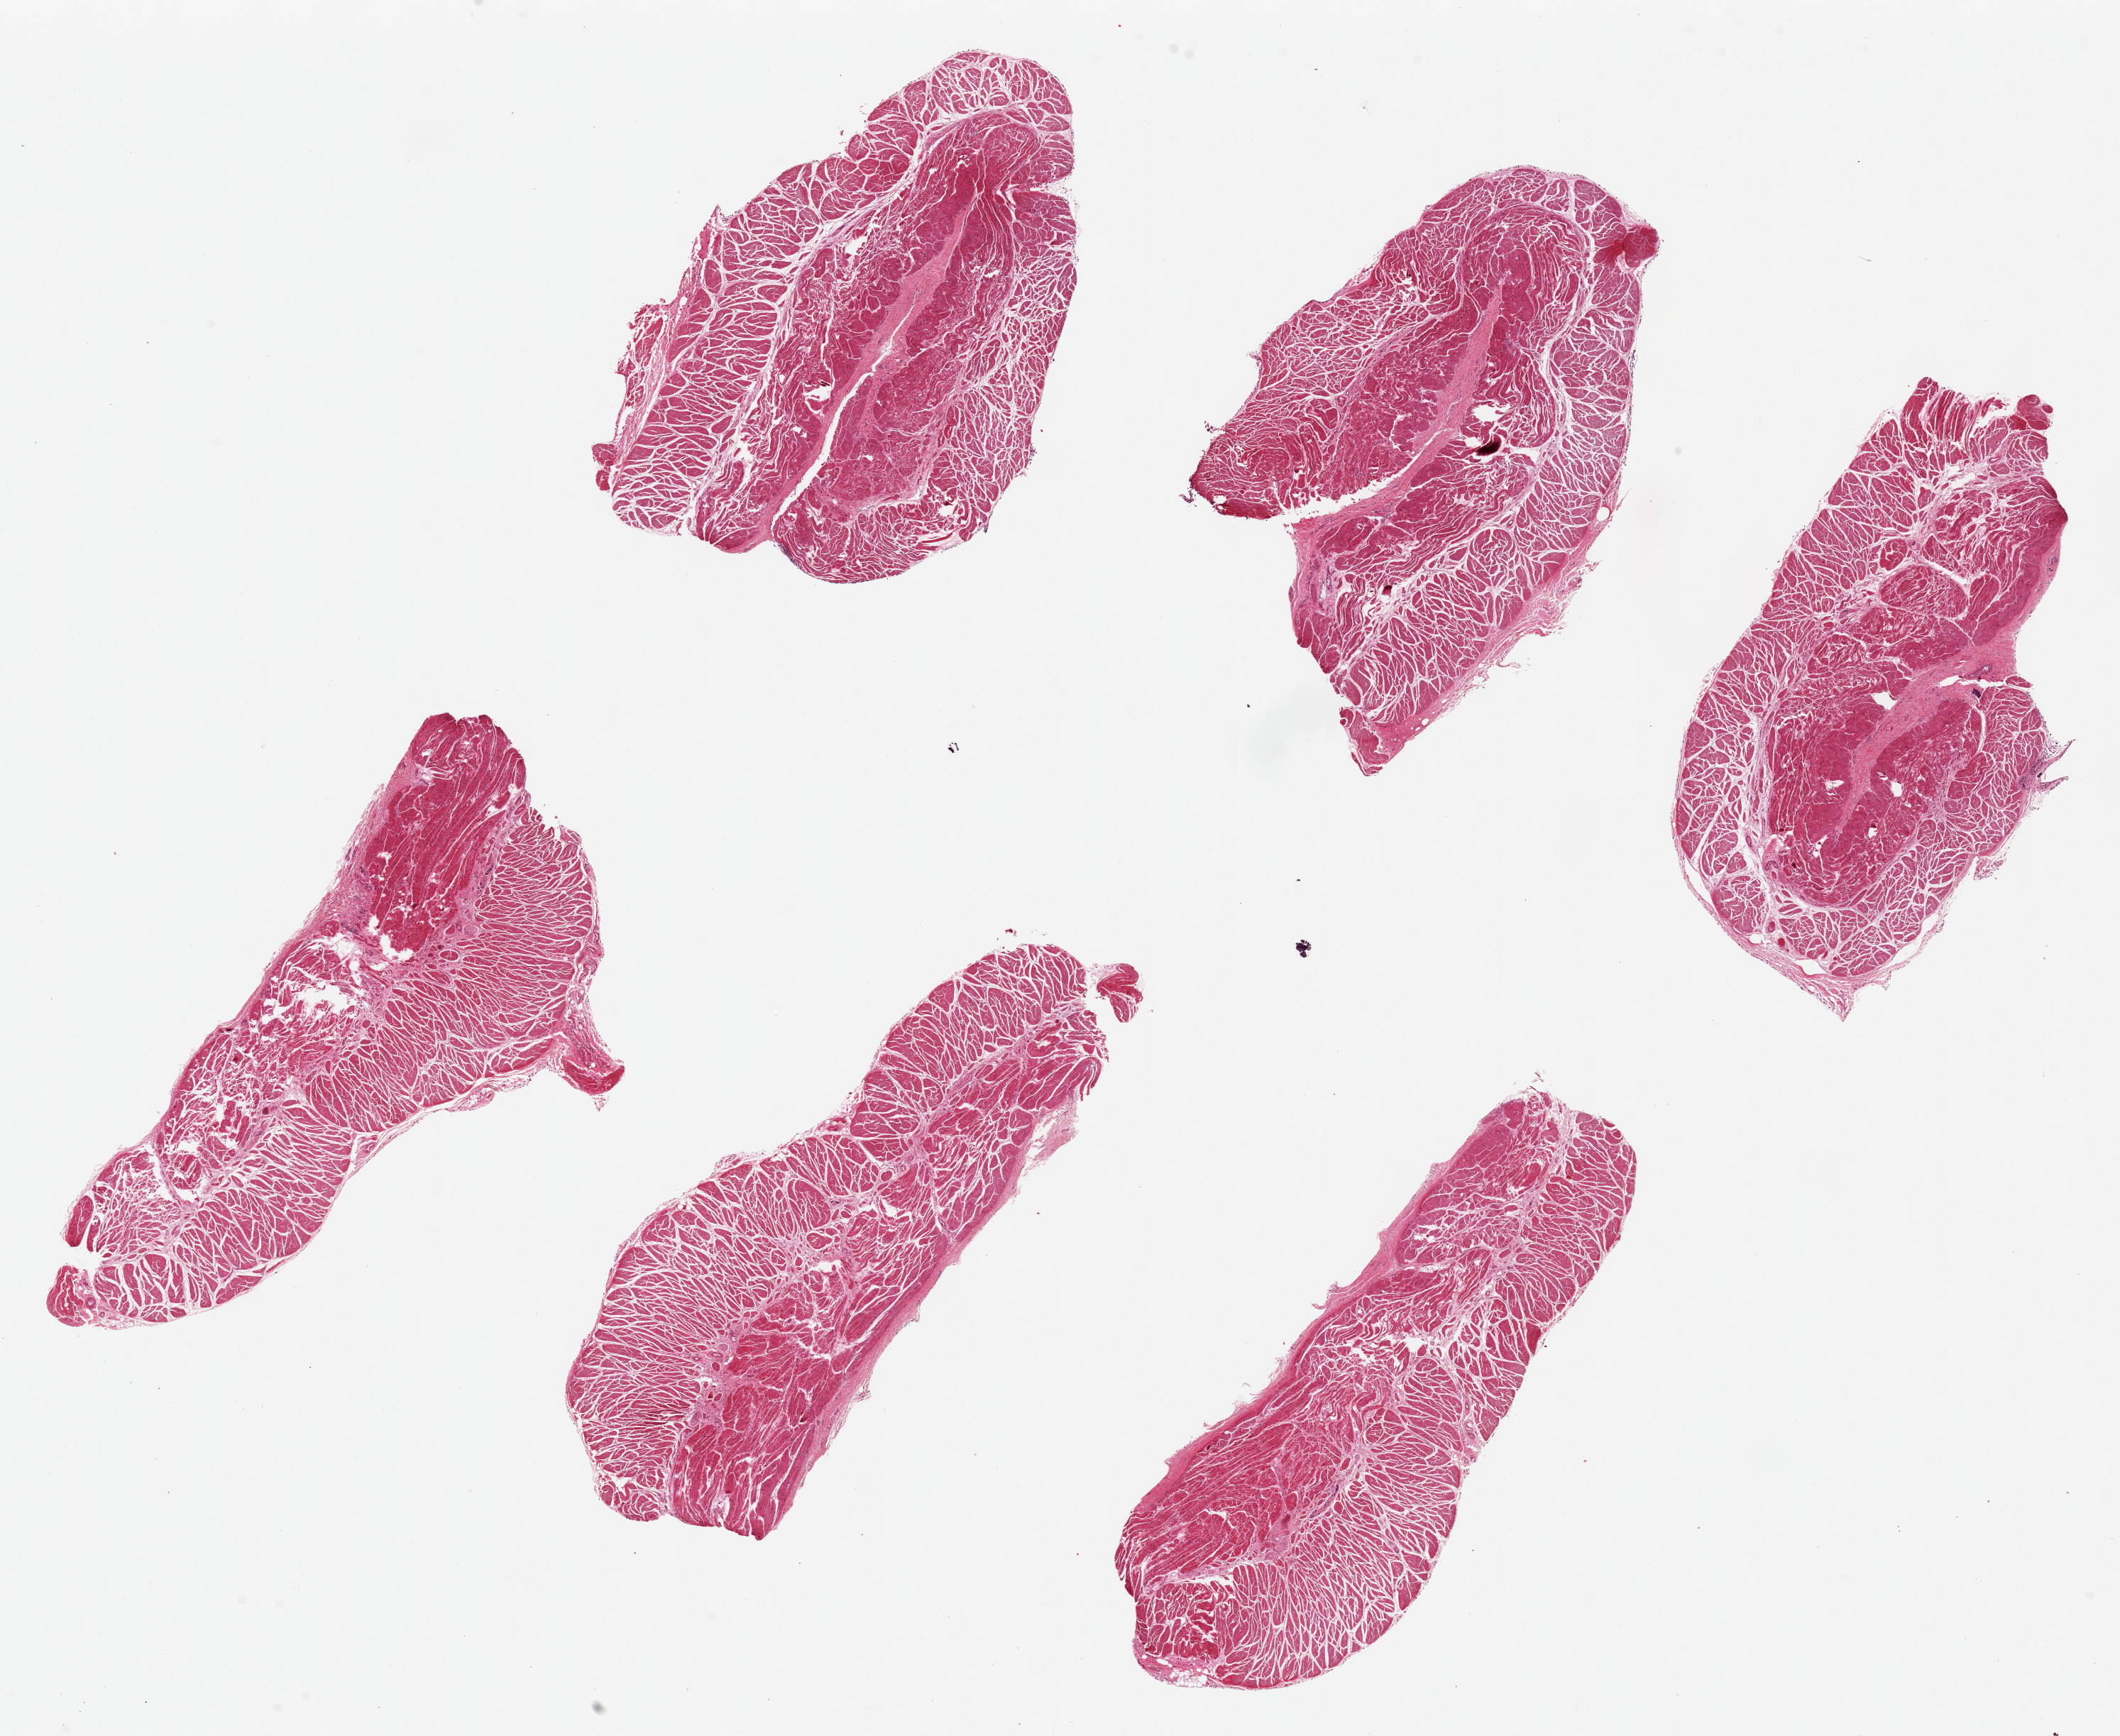
Hematoxylin and eosin (H&E) whole-slide image, a low-resolution overview of the entire scanned area, about 23.6 x 19.3 mm. PAXgene-fixed paraffin-embedded (PFPE) section. Section of esophageal muscle (target tissue). Donor tissue sample. Donor sex: male.
Review note (as recorded): 6 ~8x3mm pieces.